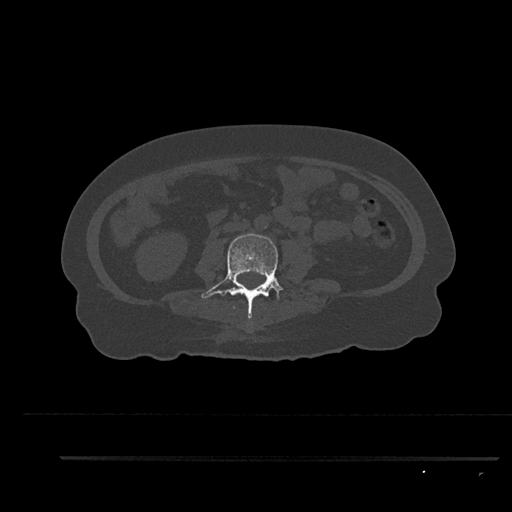
CT including the spine, one axial slice. Position 87 of 797 along the scan axis. Bone window (W 1800 / L 400 HU). 0.5 mm slice thickness. 512 × 512 image matrix, field of view 408 × 408 mm. Female patient, age 44 years. Case-level facts recorded for this patient, not image findings: primary cancer: renal; vertebrae with lytic lesions (as recorded): L1.
Annotated regions visible in this slice (semi-automatic segmentation, software-assisted and operator-edited):
- L3 vertebra: bounding box (x1, y1, x2, y2) in pixels: (201, 233, 291, 319)